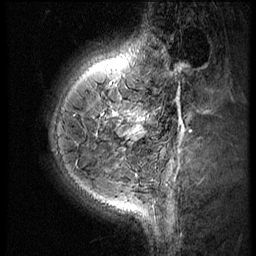
Breast MRI (dynamic contrast-enhanced), one sagittal slice. Position 16 of 60 along the scan axis. 3 images stored at this slice position (order not interpretable as contrast timing). 1.5 T. TE 4.2 ms, TR 9 ms. 256 × 256 image matrix, field of view 180 × 180 mm. Female patient, age 38 years. From the clinical record (not read from this slice): setting: breast cancer imaged before/during neoadjuvant chemotherapy; receptor status: triple-negative.
Outlined on this slice (semi-automatic segmentation, software-assisted and operator-edited):
- analysis volume of interest (the breast-tissue region the enhancement analysis was run in; not a lesion): bounding box (x1, y1, x2, y2) in pixels: (119, 93, 165, 150)
- tumour enhancement mask (voxels above the 140 % enhancement threshold inside the analysis volume of interest): (119, 112, 146, 126)